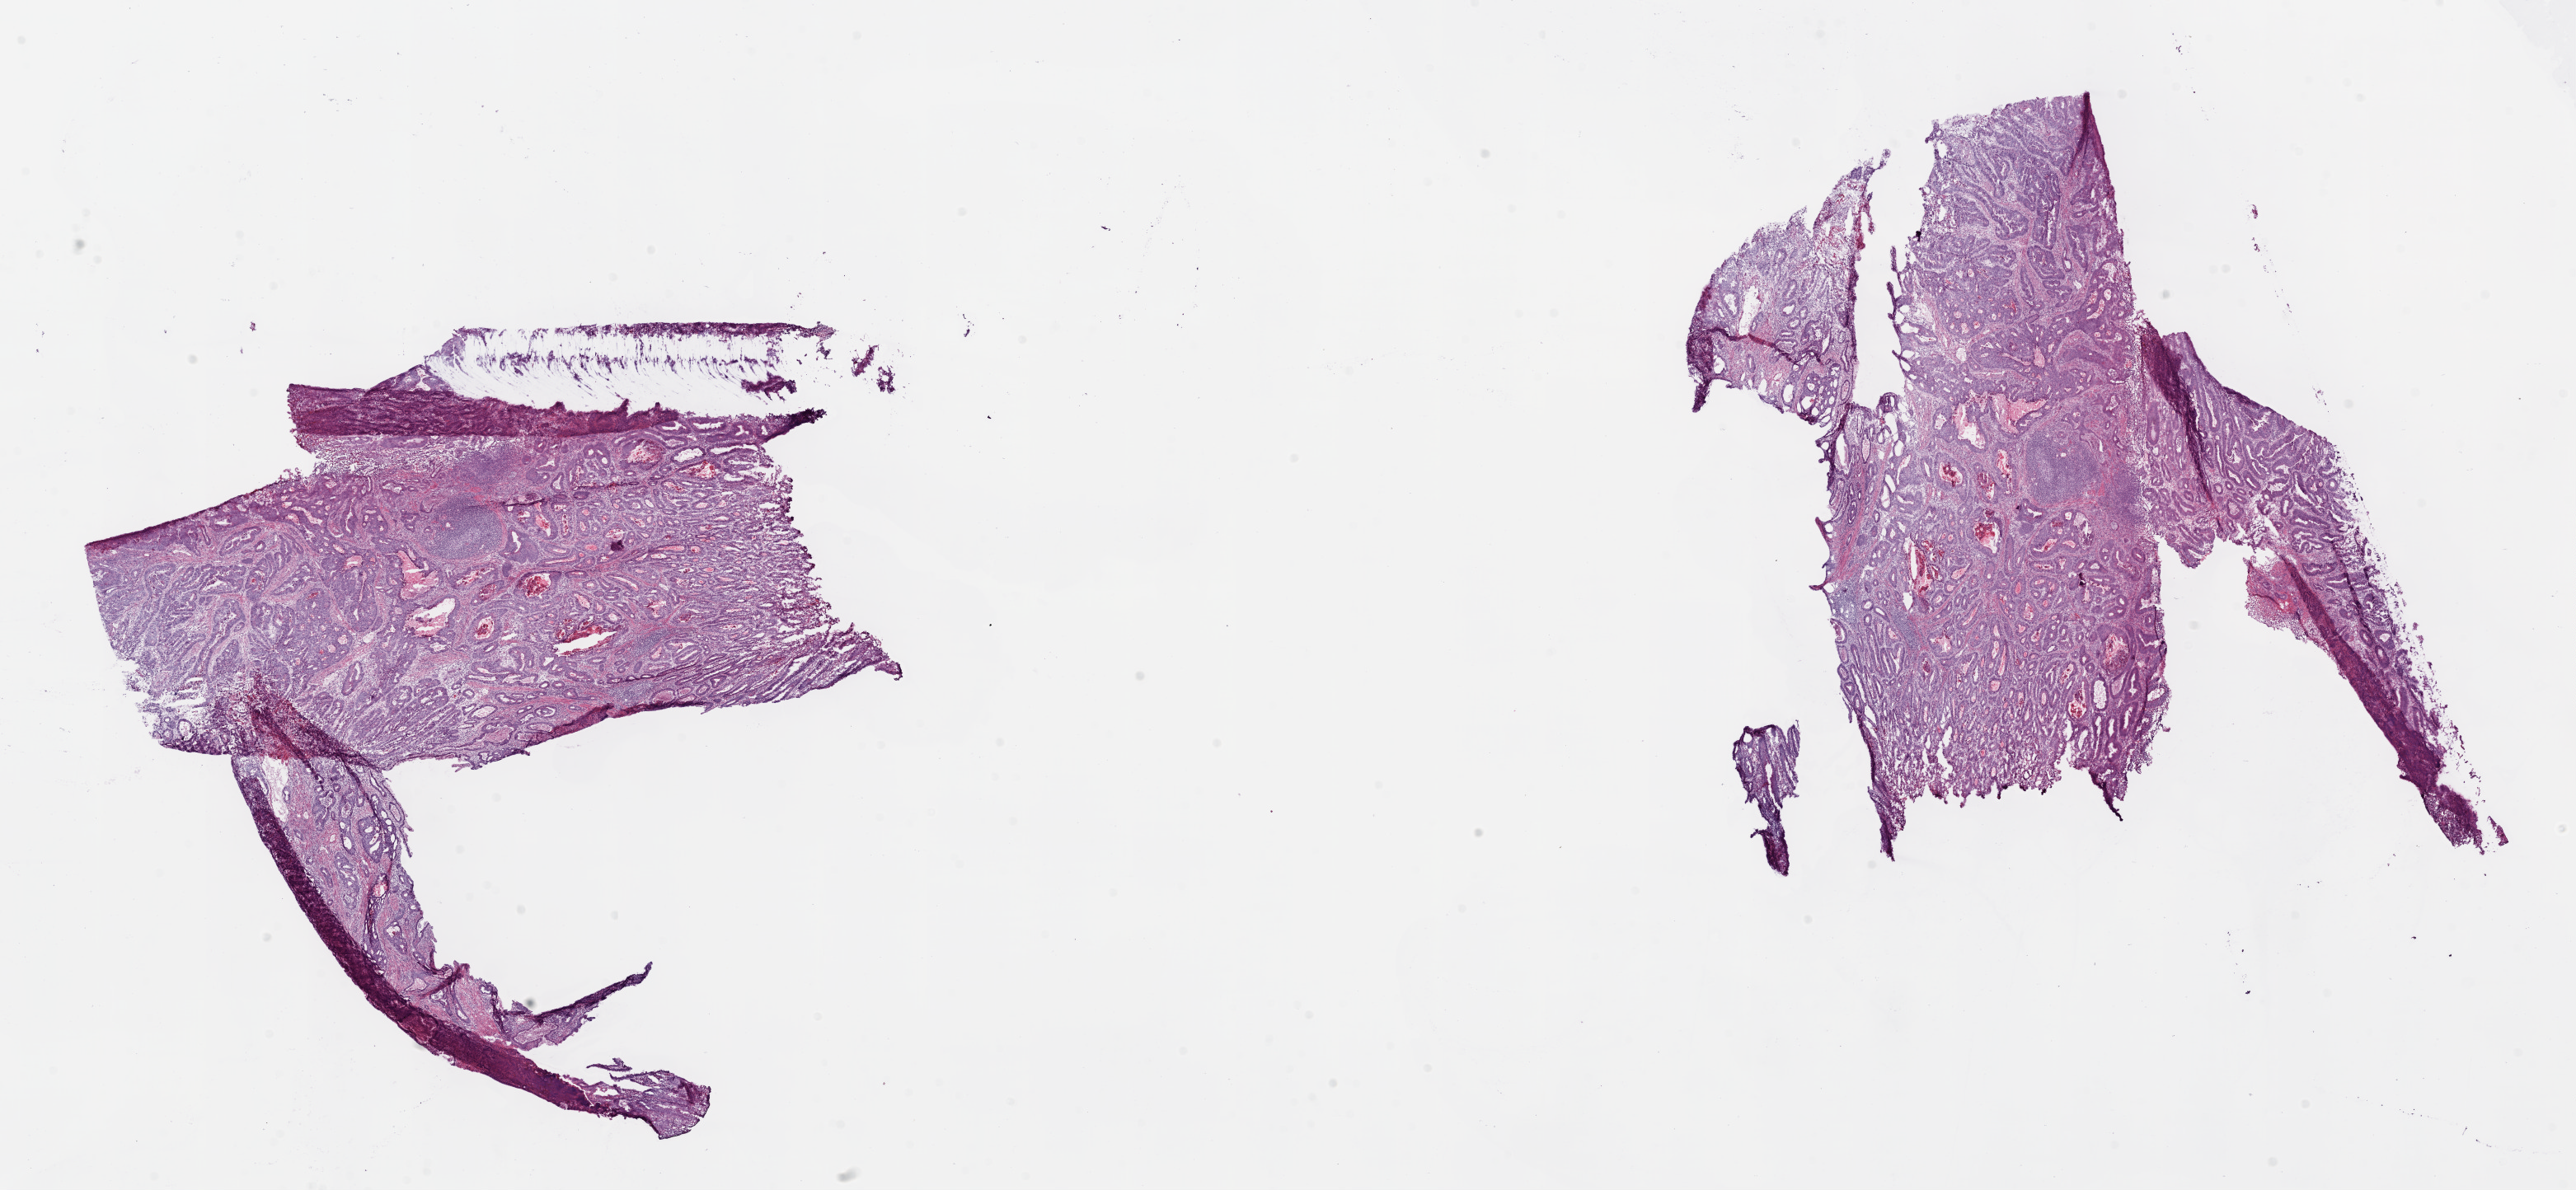
Whole-slide histology image, Hematoxylin and eosin (H&E) stained — whole scanned area (about 25.1 x 11.6 mm, slide scanned at 20x) shown as a low-resolution overview; frozen section from the bottom of the tissue portion; rectum, primary tumour sample. Patient: female, age at initial diagnosis 66 years. Slide review estimates, as recorded: tumour cells 80%, tumour nuclei 65%, stromal cells 10%, necrosis 10%. Inflammatory infiltration, as recorded: lymphocyte infiltration 20%.
- lymph nodes positive (case pathology): 0 of 18 examined
- histologic diagnosis: Adenocarcinoma, NOS
- AJCC pathologic stage: I (6th edition)